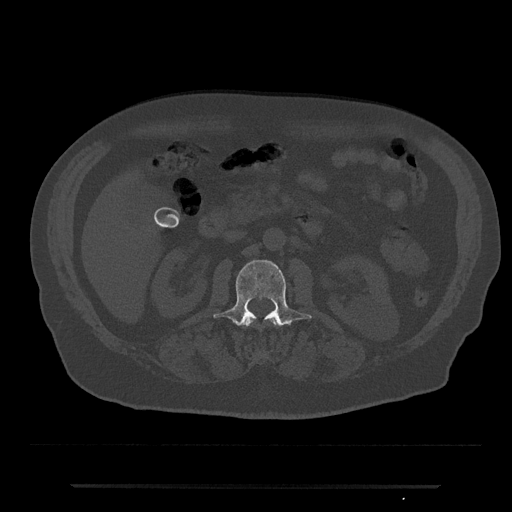
CT including the spine, one axial slice. Slice 482 of 797 in the series (ordered by position). Reconstruction kernel Br40s/3. 120 kVp. Bone window (W 1800 / L 400 HU). 512 × 512 image matrix, field of view 434 × 434 mm. Male patient, age 80 years. From the clinical record (not read from this slice): primary cancer: prostate.
Structures marked on this image (semi-automatic segmentation, software-assisted and operator-edited):
- L1 vertebra: bounding box (x1, y1, x2, y2) in pixels: (243, 318, 279, 326)
- L2 vertebra: (214, 260, 312, 326)